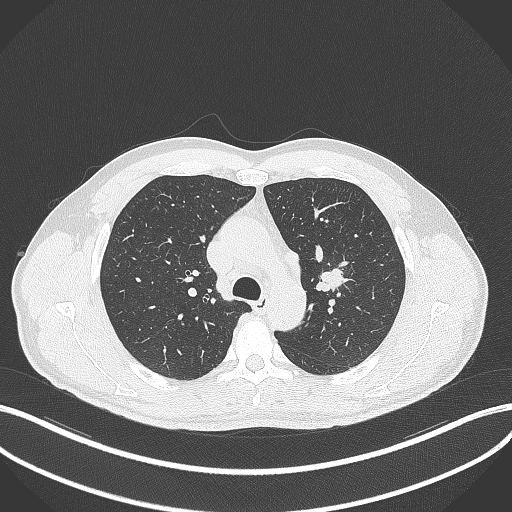
Chest CT, one axial slice; position 297 of 392 along the scan axis; reconstruction kernel B70f; 120 kVp; lung window (W 1500 / L -600 HU); 1 mm slice thickness; 512 × 512 image matrix, field of view 400 × 400 mm. Male patient, age 50 years. Case-level facts recorded for this patient, not image findings: clinical TNM (as recorded): T1c N1 M1b.
Structures marked on this image (bounding box drawn by a radiologist):
- lung tumour (recorded histology: squamous cell carcinoma): bounding box (x1, y1, x2, y2) in pixels: (313, 266, 352, 294)